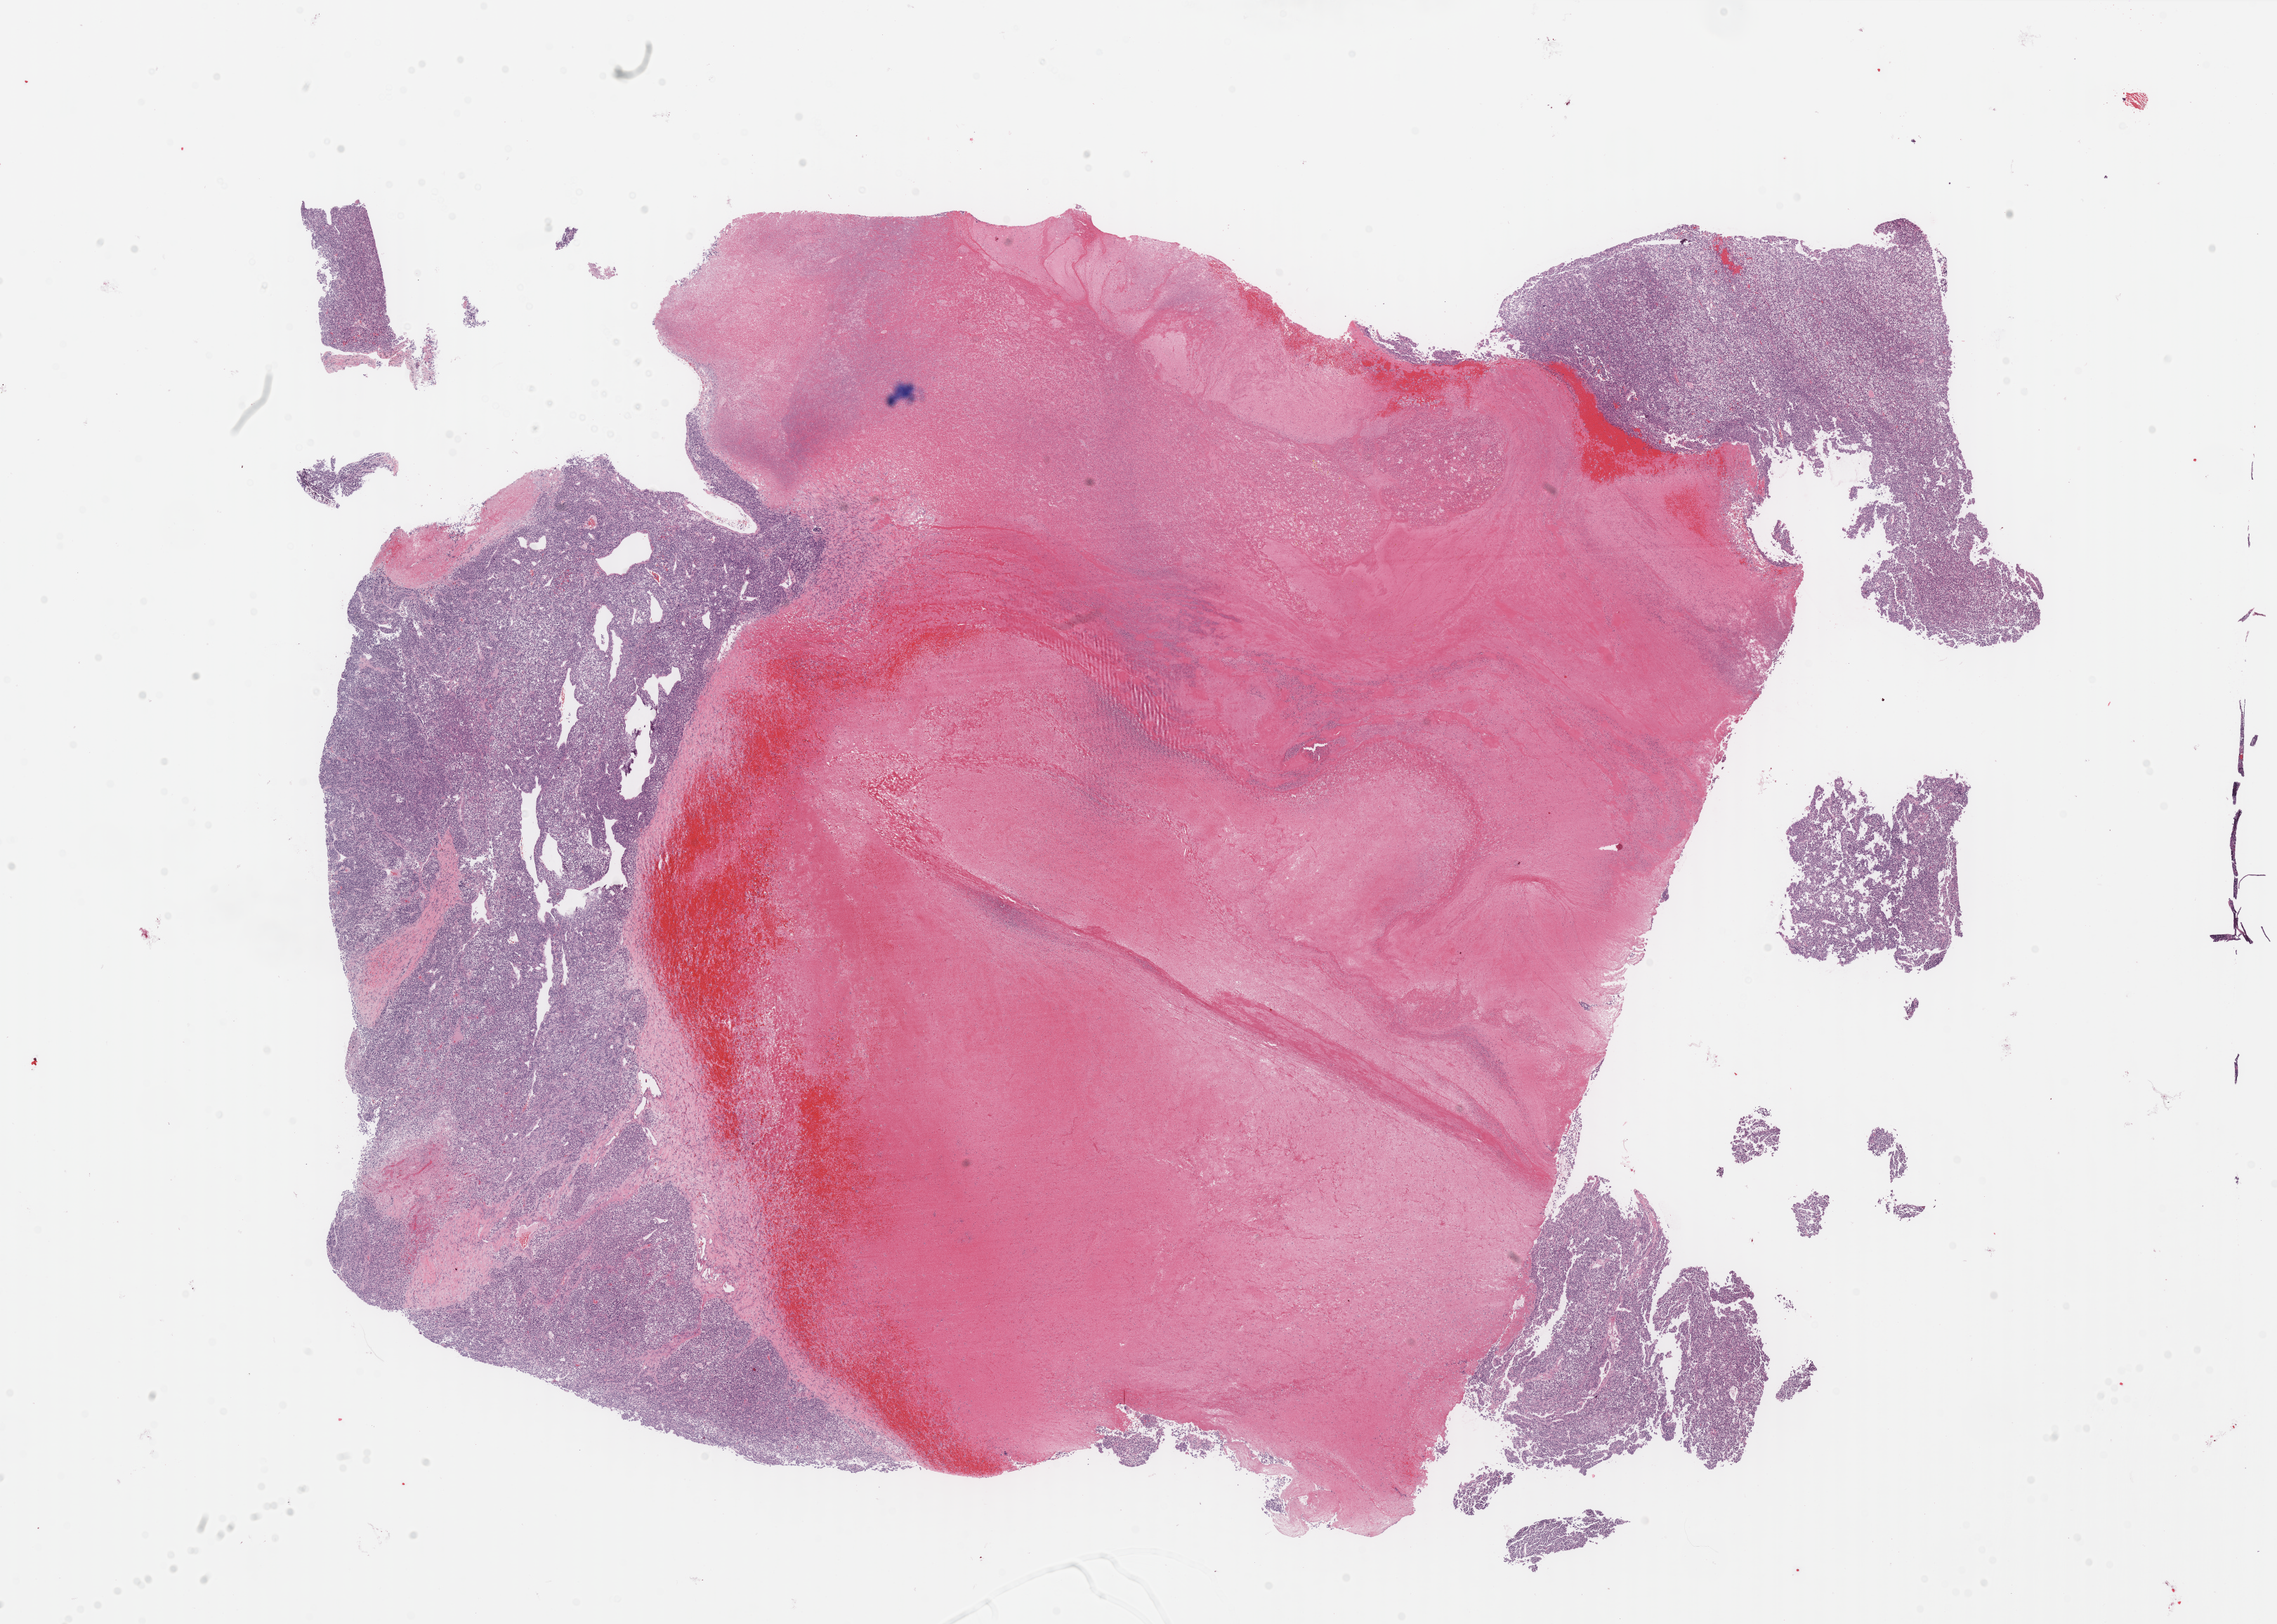
Digitized H&E-stained tissue section (whole slide), shown as a low-resolution overview of the whole scanned area (about 25.7 x 18.3 mm, acquisition: 40x scan). Formalin-fixed paraffin-embedded (FFPE) diagnostic section. Primary tumour sample from the liver. Female, age 68 years at initial diagnosis. Histologic grade: G3 (poorly differentiated).
TNM: T2 N0 M0. Histologic diagnosis: Hepatocellular carcinoma, NOS. AJCC pathologic stage: II (7th edition).